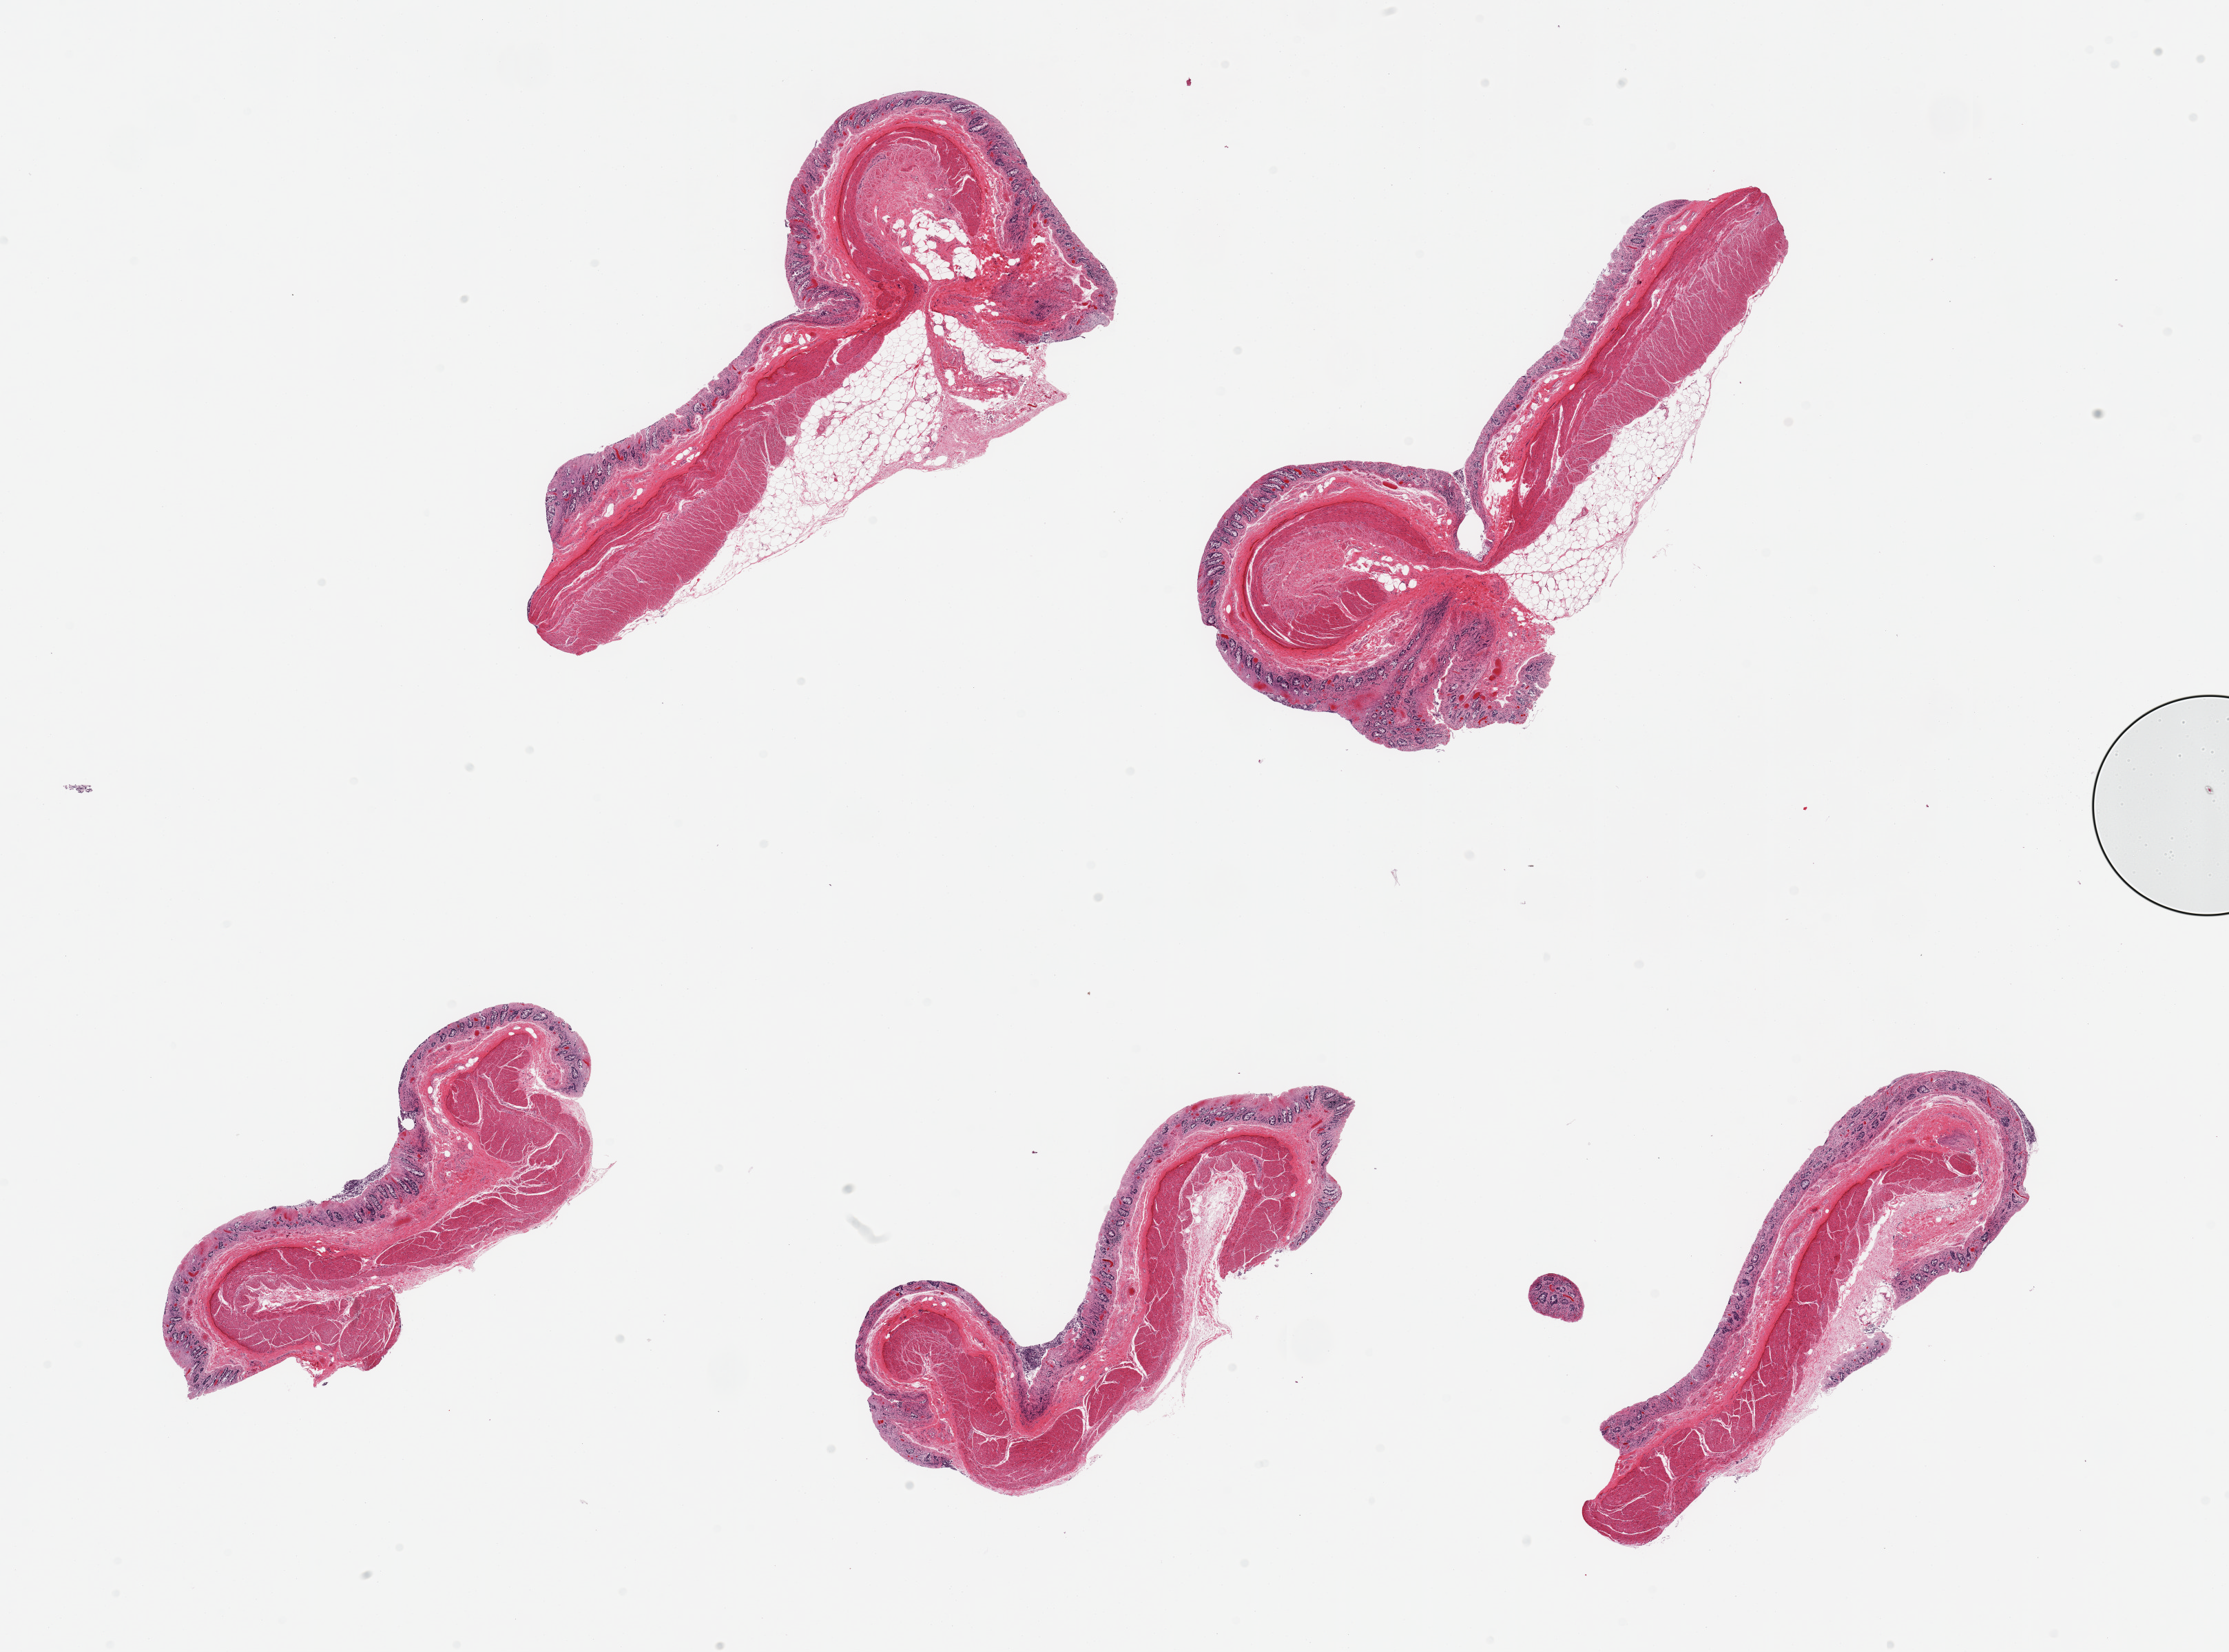
Hematoxylin and eosin (H&E) whole-slide image, a low-resolution overview of the entire scanned area, about 25.6 x 19.0 mm. PAXgene-fixed paraffin-embedded (PFPE) section. Section of transverse colon (target tissue). Tissue donor sample. Male donor.
• reviewer comment on this tissue sample: 5 pieces; full thickness, few with attached fat, diverticulum, mucosa is moderately to severely autolyzed